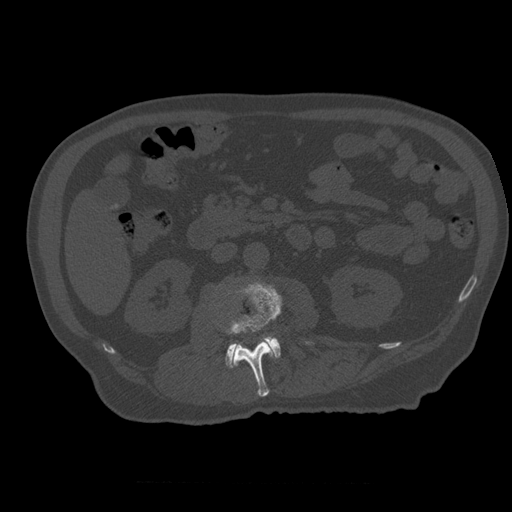
CT including the spine, one axial slice. Reconstruction kernel STANDARD. 120 kVp. Bone window (W 1800 / L 400 HU). 1.25 mm slice thickness. 512 × 512 image matrix, field of view 407 × 407 mm. Patient age 73 years. Case-level facts recorded for this patient, not image findings: primary cancer: prostate; vertebrae with lytic lesions (as recorded): L2.
Annotated regions visible in this slice (semi-automatic segmentation, software-assisted and operator-edited):
- L2 vertebra: box from (x=226, y=283) to (x=282, y=397) px
- L3 vertebra: (x=226, y=337)–(x=281, y=367)